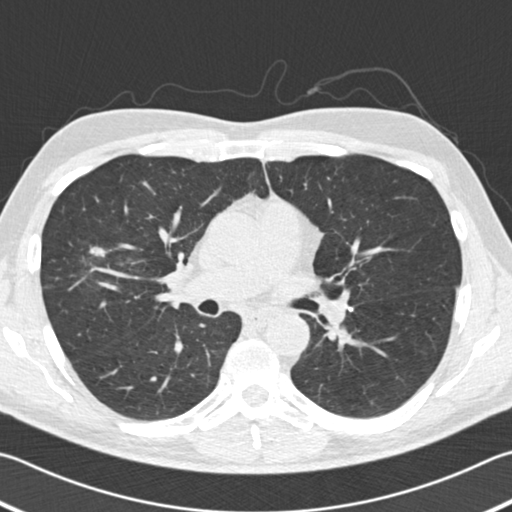
Low-dose screening chest CT, one axial slice. Position 109 of 182 along the scan axis. Reconstruction kernel B30f. Lung window (W 1500 / L -600 HU). 2 mm slice thickness. 512 × 512 image matrix, field of view 344 × 344 mm.
Annotated regions visible in this slice (manually delineated by an expert):
- lesion 1 (tumor, upper lobe of right lung): box from (x=89, y=247) to (x=106, y=257) px